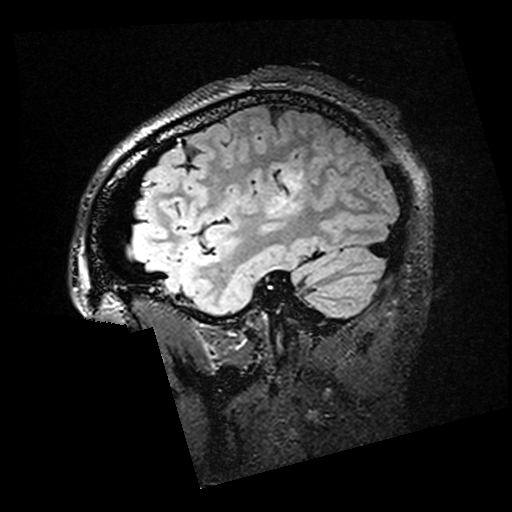
Brain MRI from a brain-tumour surgery series, one sagittal slice; slice 43 of 176 in the series (ordered by position); T2 FLAIR; 1 mm slice thickness; 512 × 512 image matrix, field of view 250 × 250 mm. From the clinical record (not read from this slice): histopathology: Oligodendroglioma; WHO grade: 2; IDH mutation: yes.
Structures marked on this image (manually delineated by an expert):
- residual tumour: bounding box <282,174,303,190> (left, top, right, bottom; pixels)